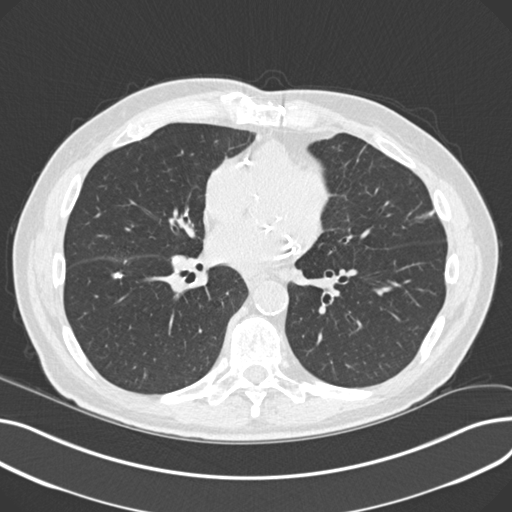
Low-dose screening chest CT, one axial slice; slice 98 of 230 in the series (ordered by position); reconstruction kernel B30f; 120 kVp; lung window (W 1500 / L -600 HU); 2 mm slice thickness; 512 × 512 image matrix, field of view 372 × 372 mm.
Structures marked on this image (expert manual segmentation):
- lesion 2 (tumor, lower lobe of right lung): bounding box (x1, y1, x2, y2) in pixels: (113, 272, 122, 279)